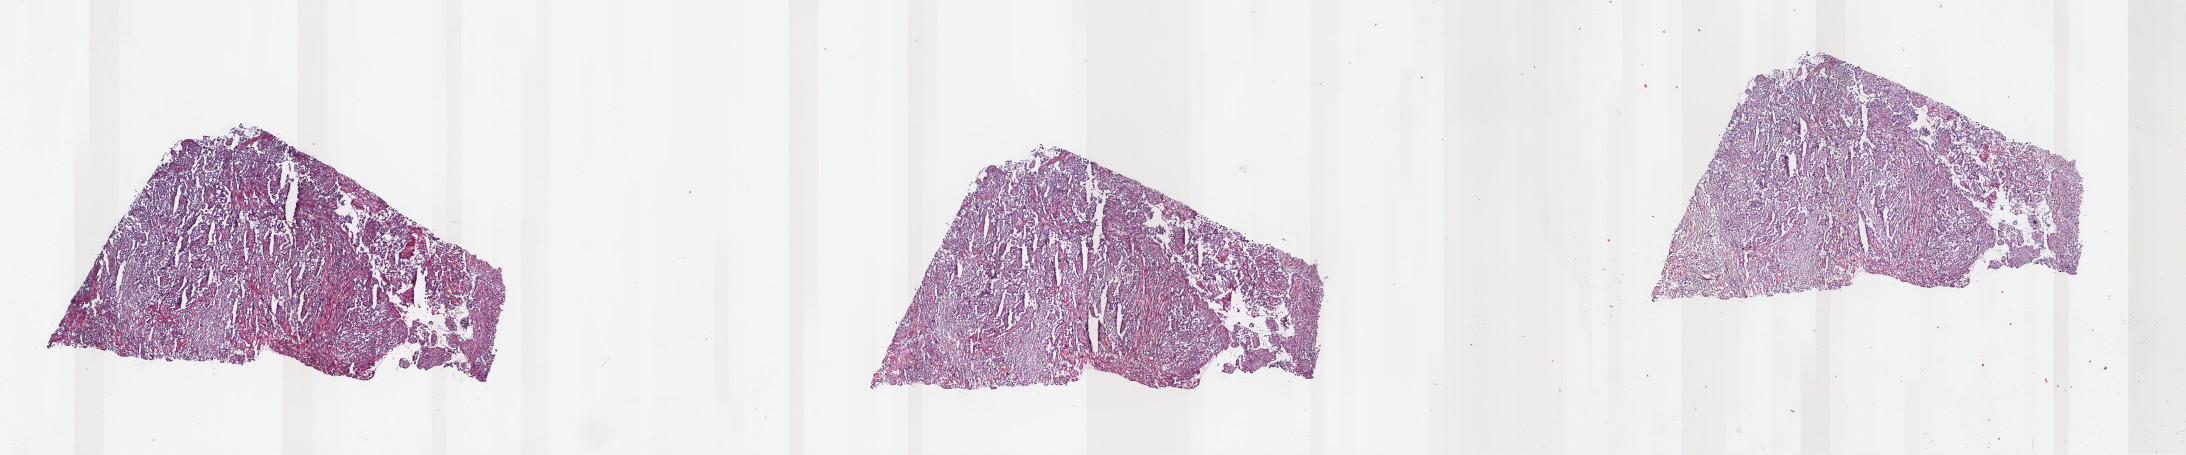
Whole-slide histology image, H&E — a low-resolution overview of the entire scanned area, about 34.4 x 7.2 mm (from a 40x scan); frozen section; mesothelium, primary tumour sample. Male patient; age at initial diagnosis 64 years. Composition of this section per pathologist review: tumour cells 100%, tumour nuclei 75%, normal cells 0%, stromal cells 0%, necrosis 0%. Infiltration values recorded for this section: lymphocyte infiltration 0%, monocyte infiltration 0%, neutrophil infiltration 0%.
- AJCC pathologic stage: III
- pathologic diagnosis: Epithelioid mesothelioma, malignant (pleura, NOS)